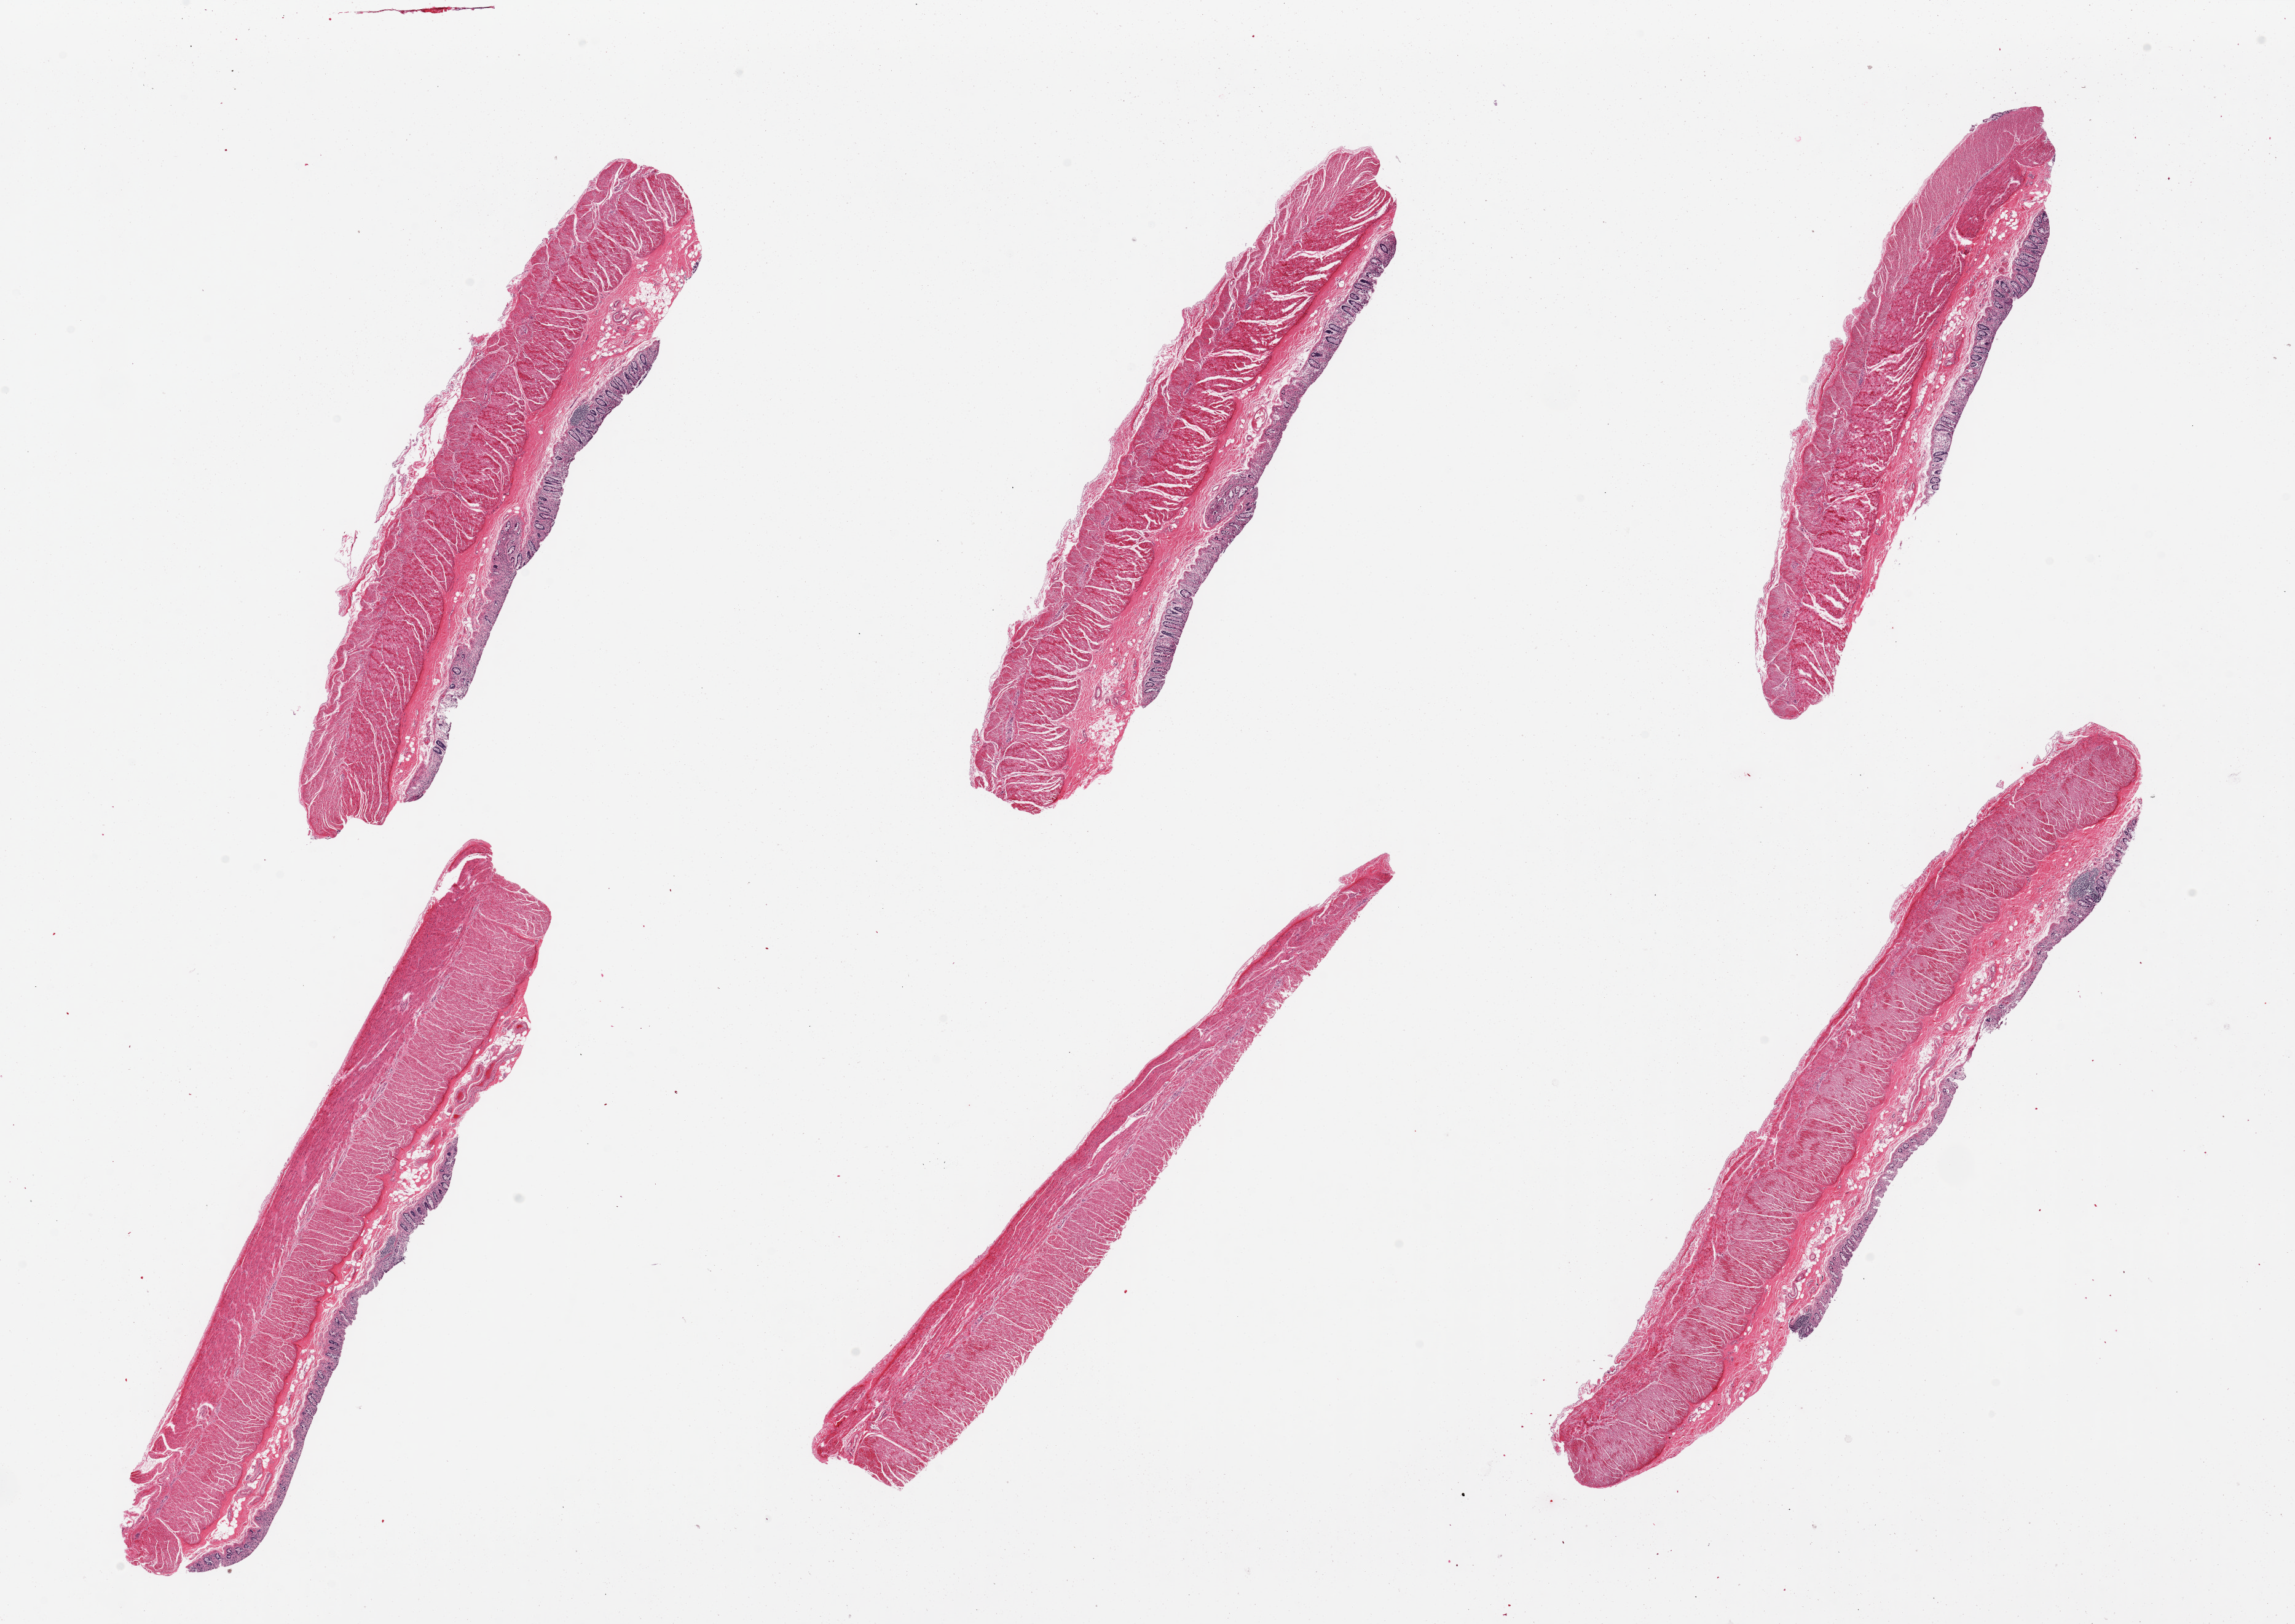
H&E whole-slide image — shown as a low-resolution overview of the whole scanned area (about 29.5 x 20.9 mm); PAXgene-fixed paraffin-embedded (PFPE) section; section of transverse colon (target tissue); donor tissue sample. Female donor.
Review note (as recorded): 6 pieces, mucosa moderately-severely autolzyed, ~300 micrions thick.